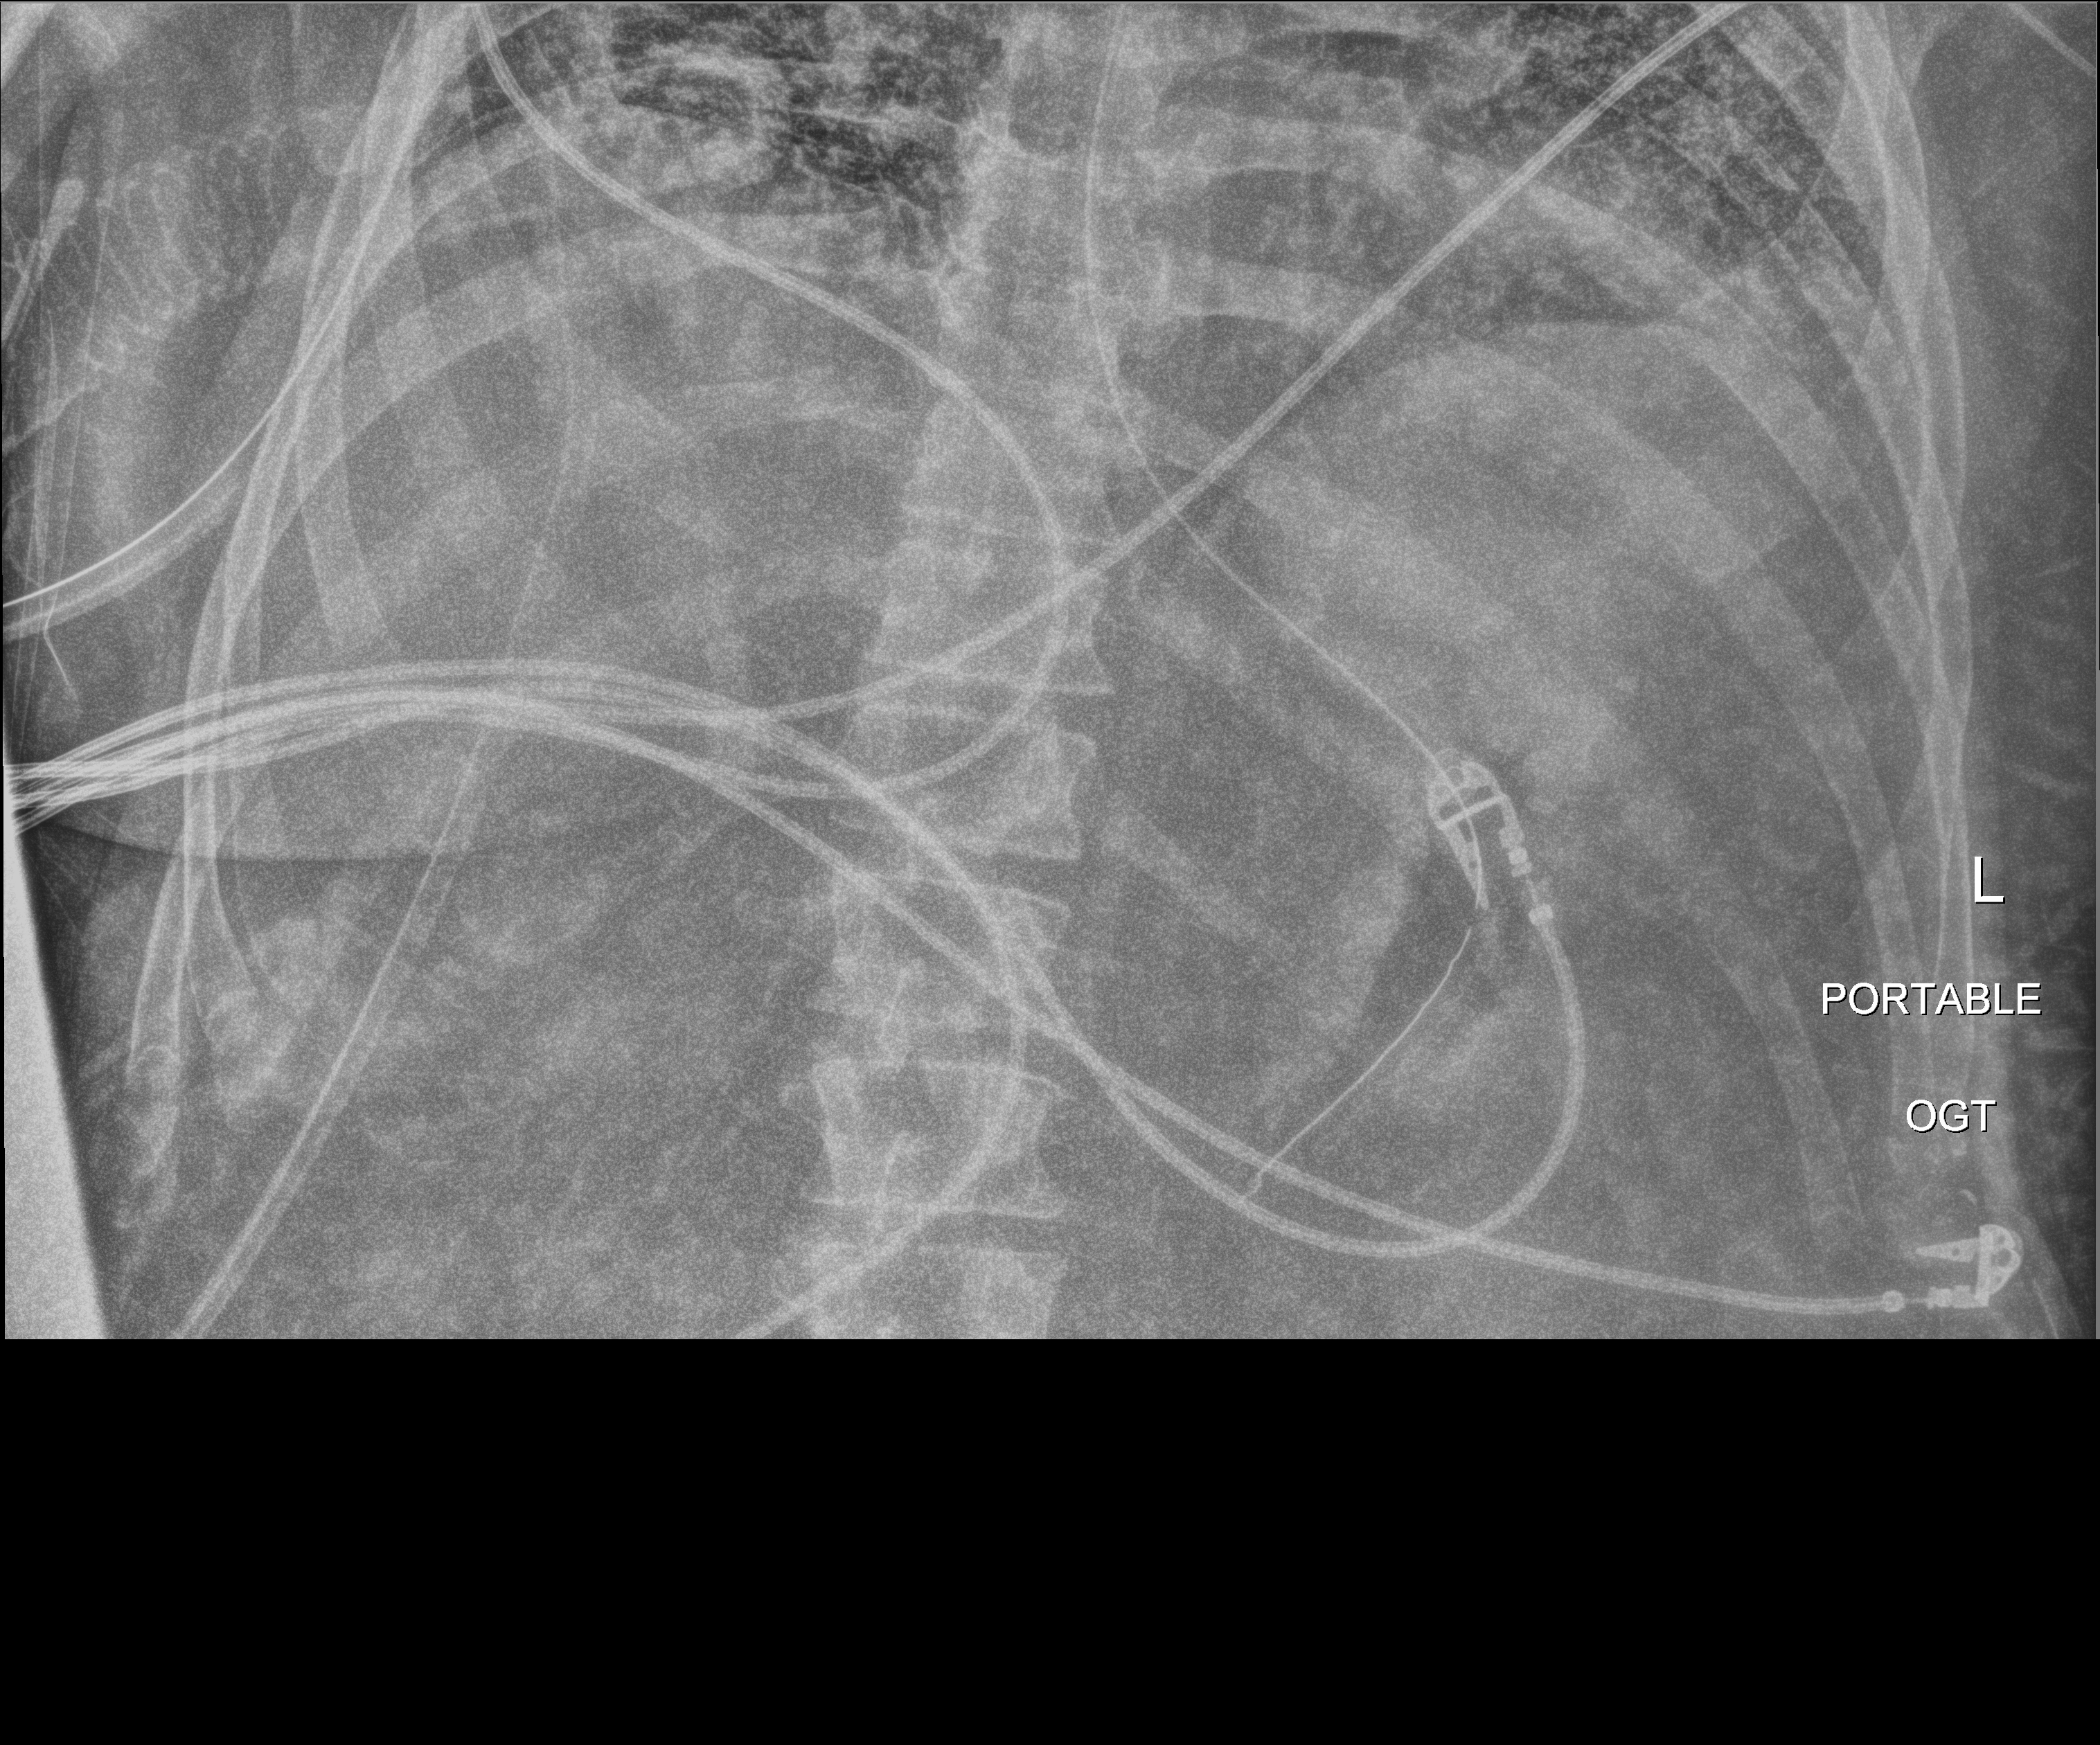
Chest radiograph; anteroposterior (AP) projection. Patient hospitalised with COVID-19; male, aged 18–59 years.
From the hospital-stay record, not from the radiograph (when in the stay this image was taken is not recorded):
- admitted to intensive care during this hospital stay: yes
- mechanically ventilated during this hospital stay: yes